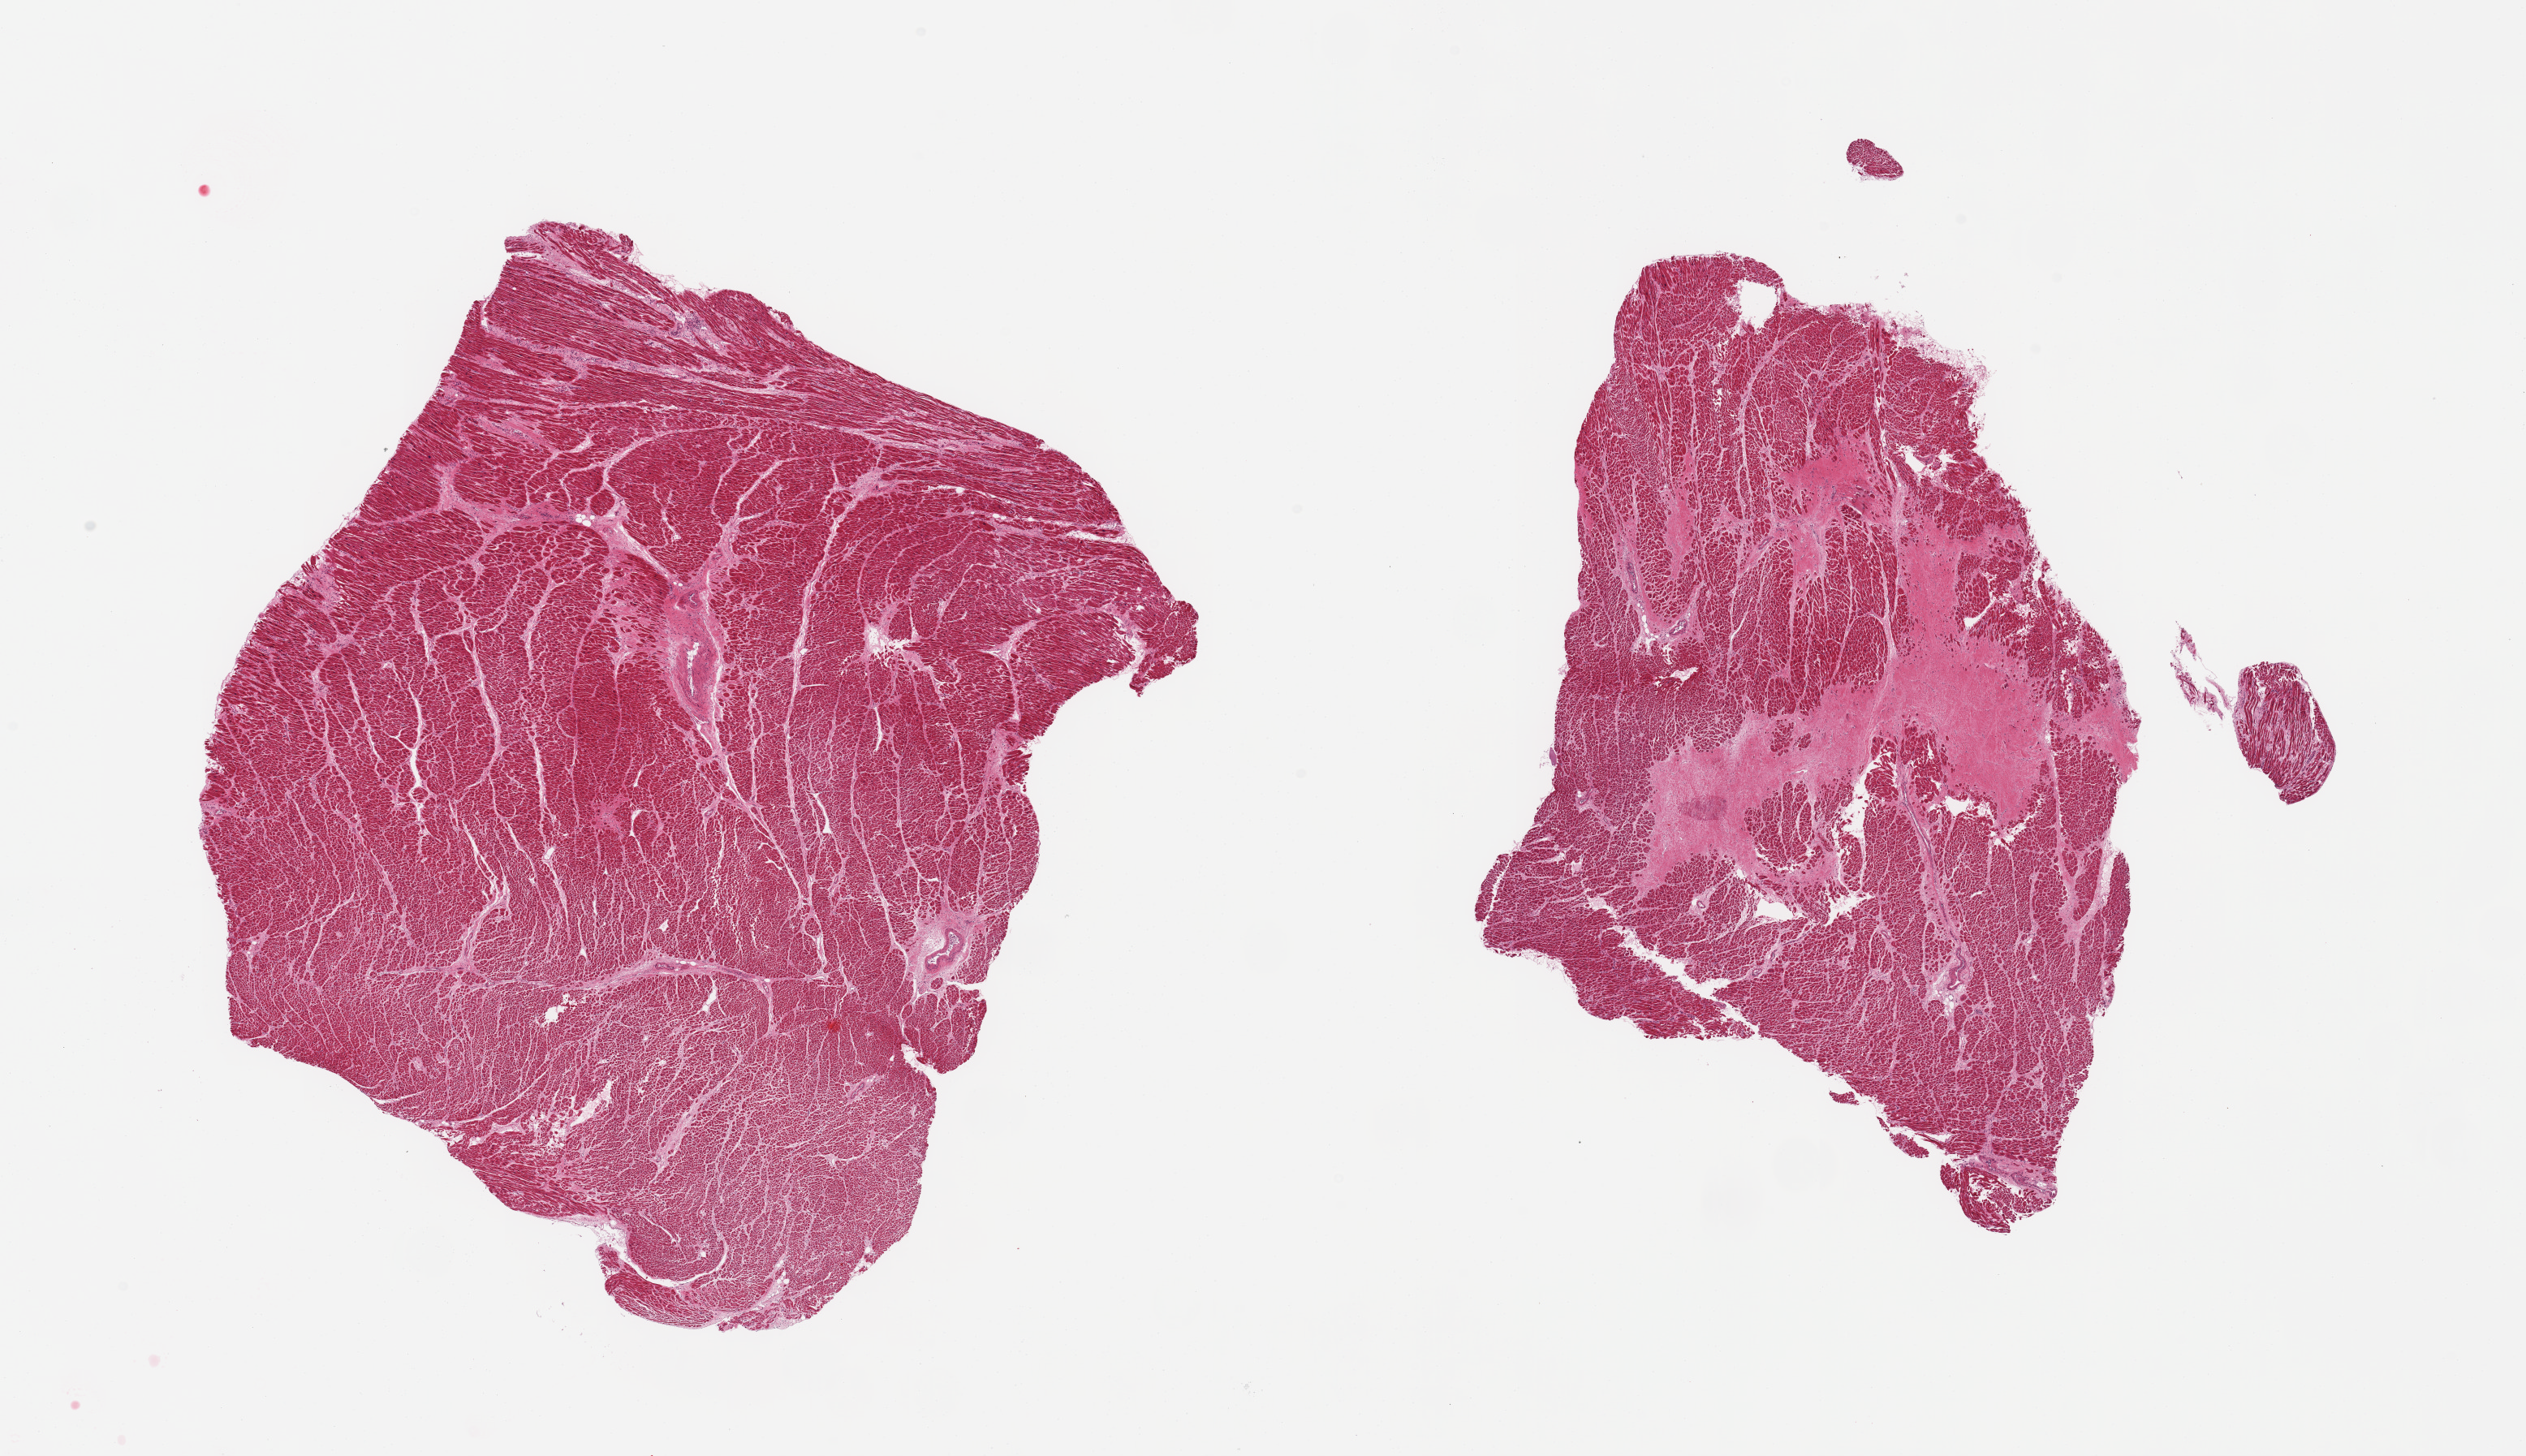
Whole-slide image, H&E stain — shown as a low-resolution overview of the whole scanned area (about 24.6 x 14.2 mm), PAXgene-fixed paraffin-embedded (PFPE) section, target tissue: heart, donor tissue sample. Donor sex: female.
Pathologist's review note for this sample: 2 pieces; extensive area of infarct (1 piece - recent and remote), interstitial fibrosis and hypertrophy.